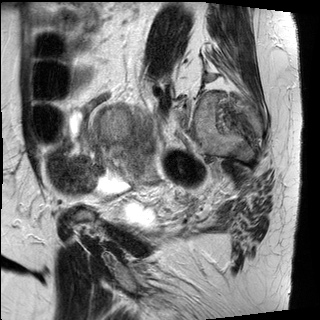
Pelvic MRI for cervical cancer, one sagittal slice. Position 23 of 30 along the scan axis. T2-weighted. 1.5 T. TE 89 ms, TR 2930 ms. 4 mm slice thickness. 320 × 320 image matrix. Patient: female, 62 years.
Outlined on this slice (expert manual segmentation):
- uterus and cervix: bounding box (x1, y1, x2, y2) in pixels: (95, 103, 158, 172)